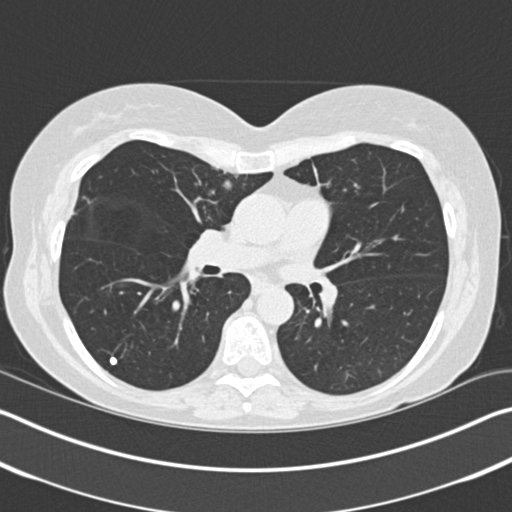
Chest CT (low-dose screening protocol), one axial image; first (baseline) screen; lung window (W 1500 / L -600 HU); 2 mm slice thickness; slice 84 of 183 in the series; 512 × 512 image matrix, field of view 340 × 340 mm. Female participant, aged 61 years at enrolment. Former smoker at enrolment.
Lesion marked by an expert reader, bounding box (x1, y1, x2, y2) in pixels: (202, 168, 244, 207). The screening reader recorded 2 non-calcified nodules or masses ≥4 mm on this exam (right upper lobe, right upper lobe); which of them this box marks is not recorded. Later outcome: lung cancer diagnosed 131 days after this screen — adenocarcinoma, NOS, right upper lobe, stage IA (AJCC 6th edition), 11 mm at pathology.